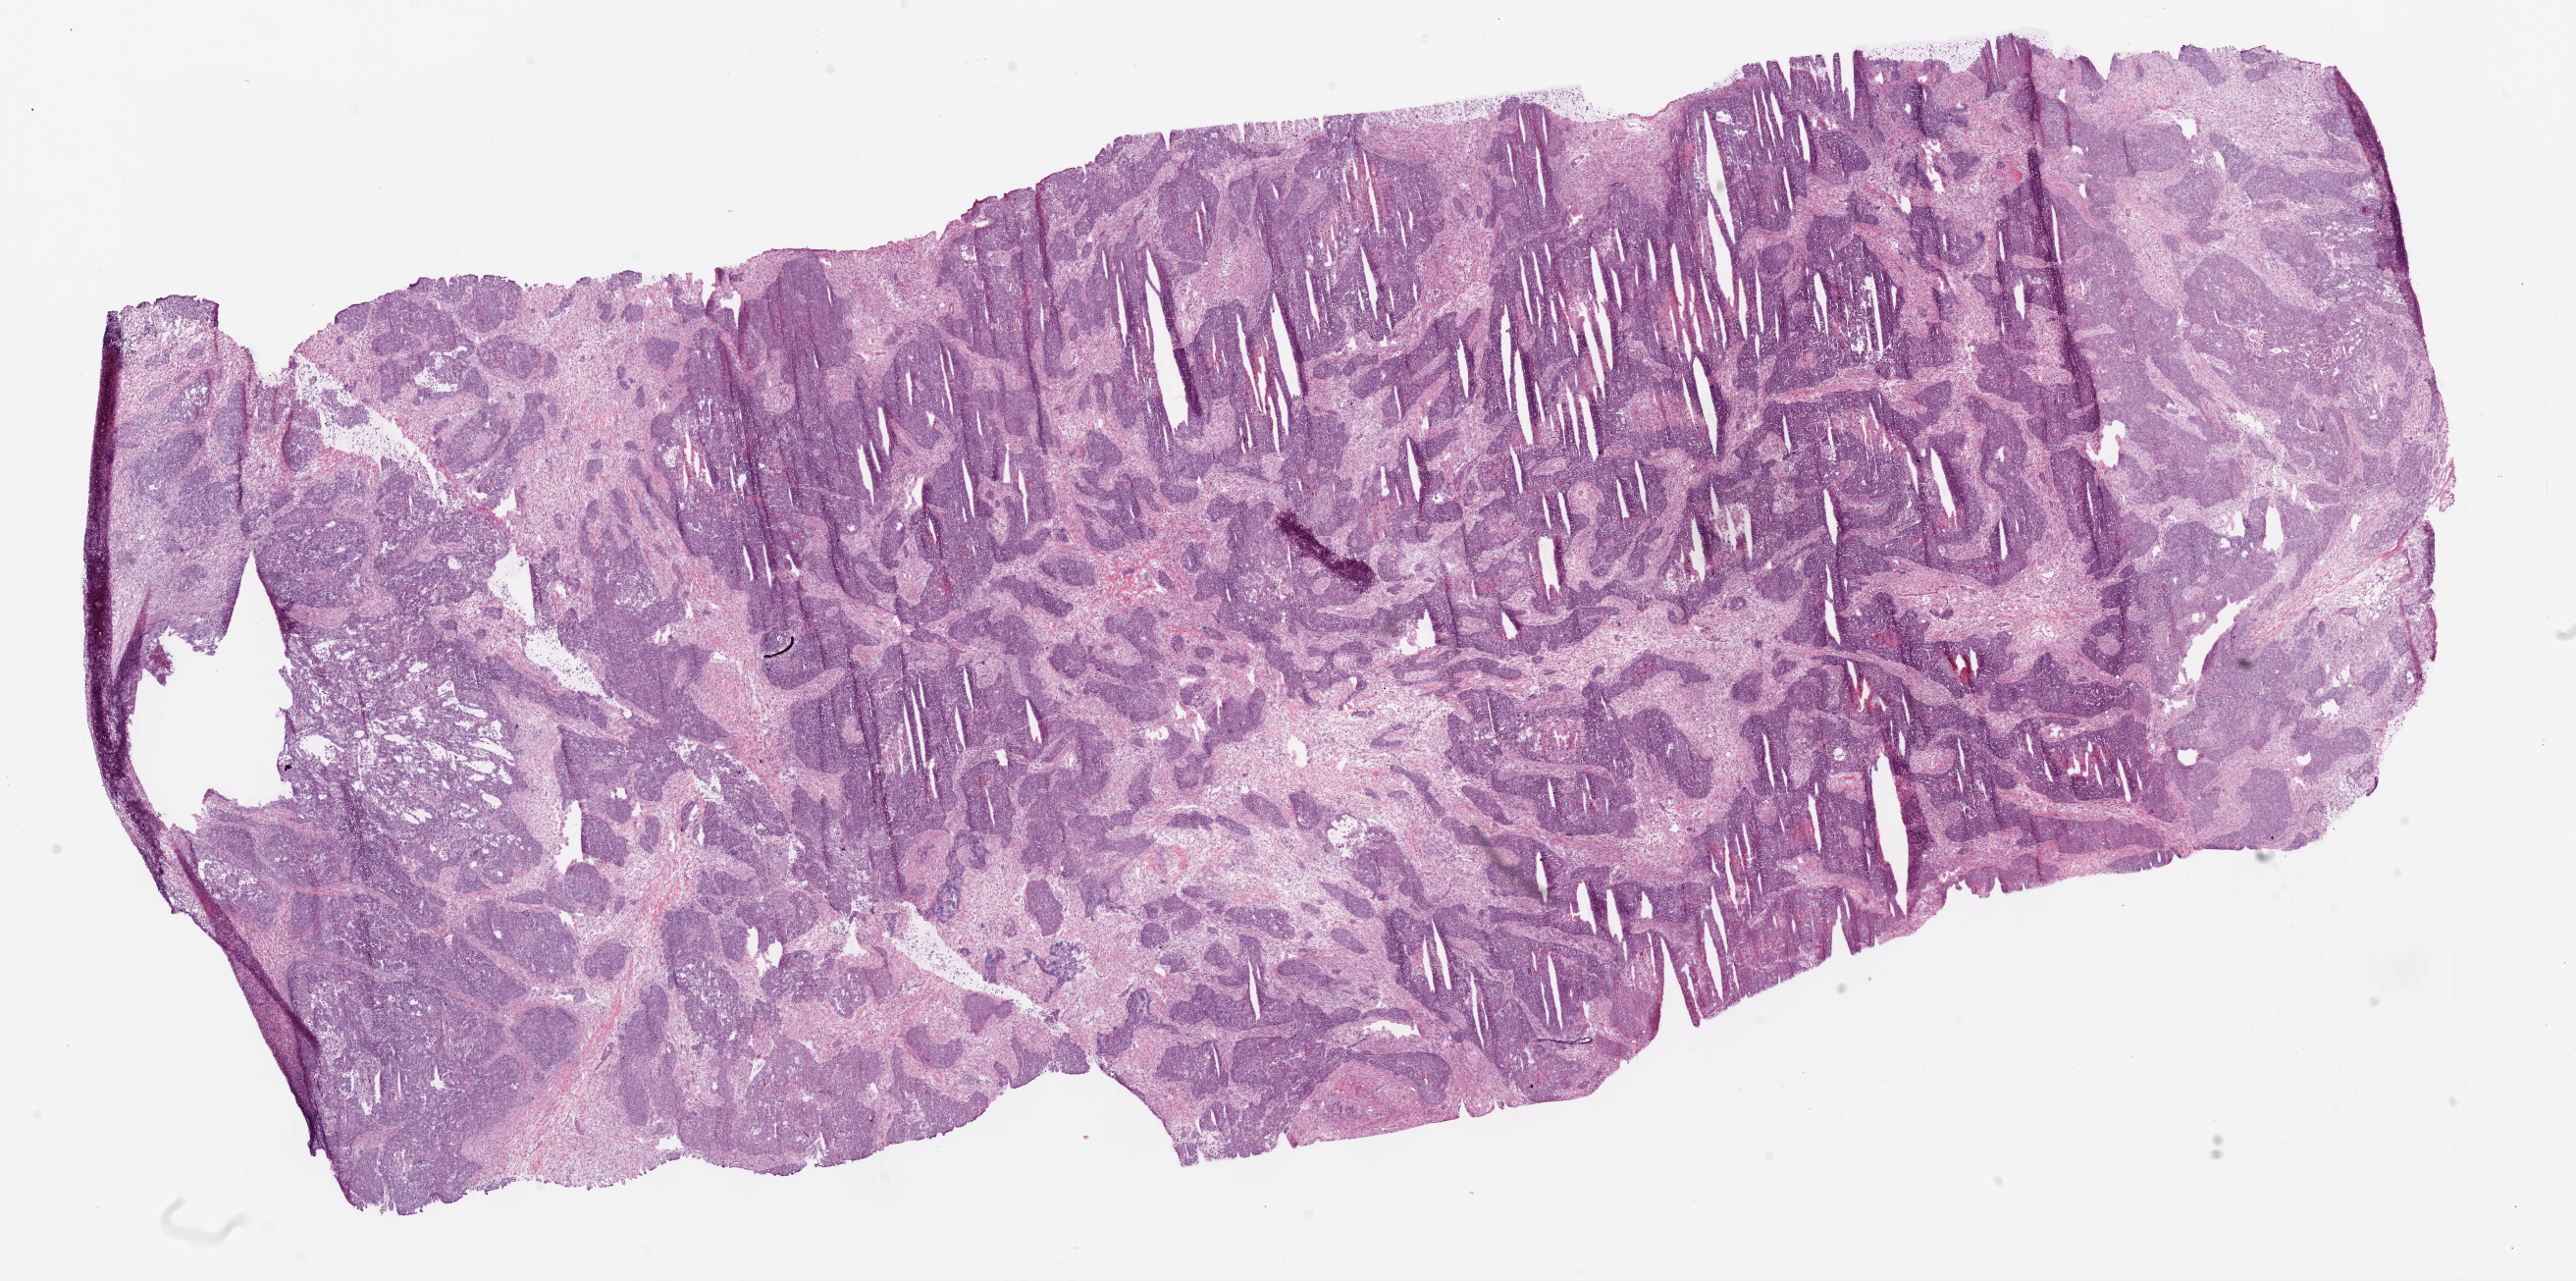
Whole-slide histology image, H&E-stained — low-resolution overview of the scanned area, about 21.1 x 10.5 mm; frozen section from the bottom of the tissue portion; ovary, primary tumour sample. Female patient; age at initial diagnosis 71 years. Composition of this section per pathologist review: tumour cells 60%, tumour nuclei 70%.
Diagnosis: Serous cystadenocarcinoma, NOS (peritoneum, NOS).